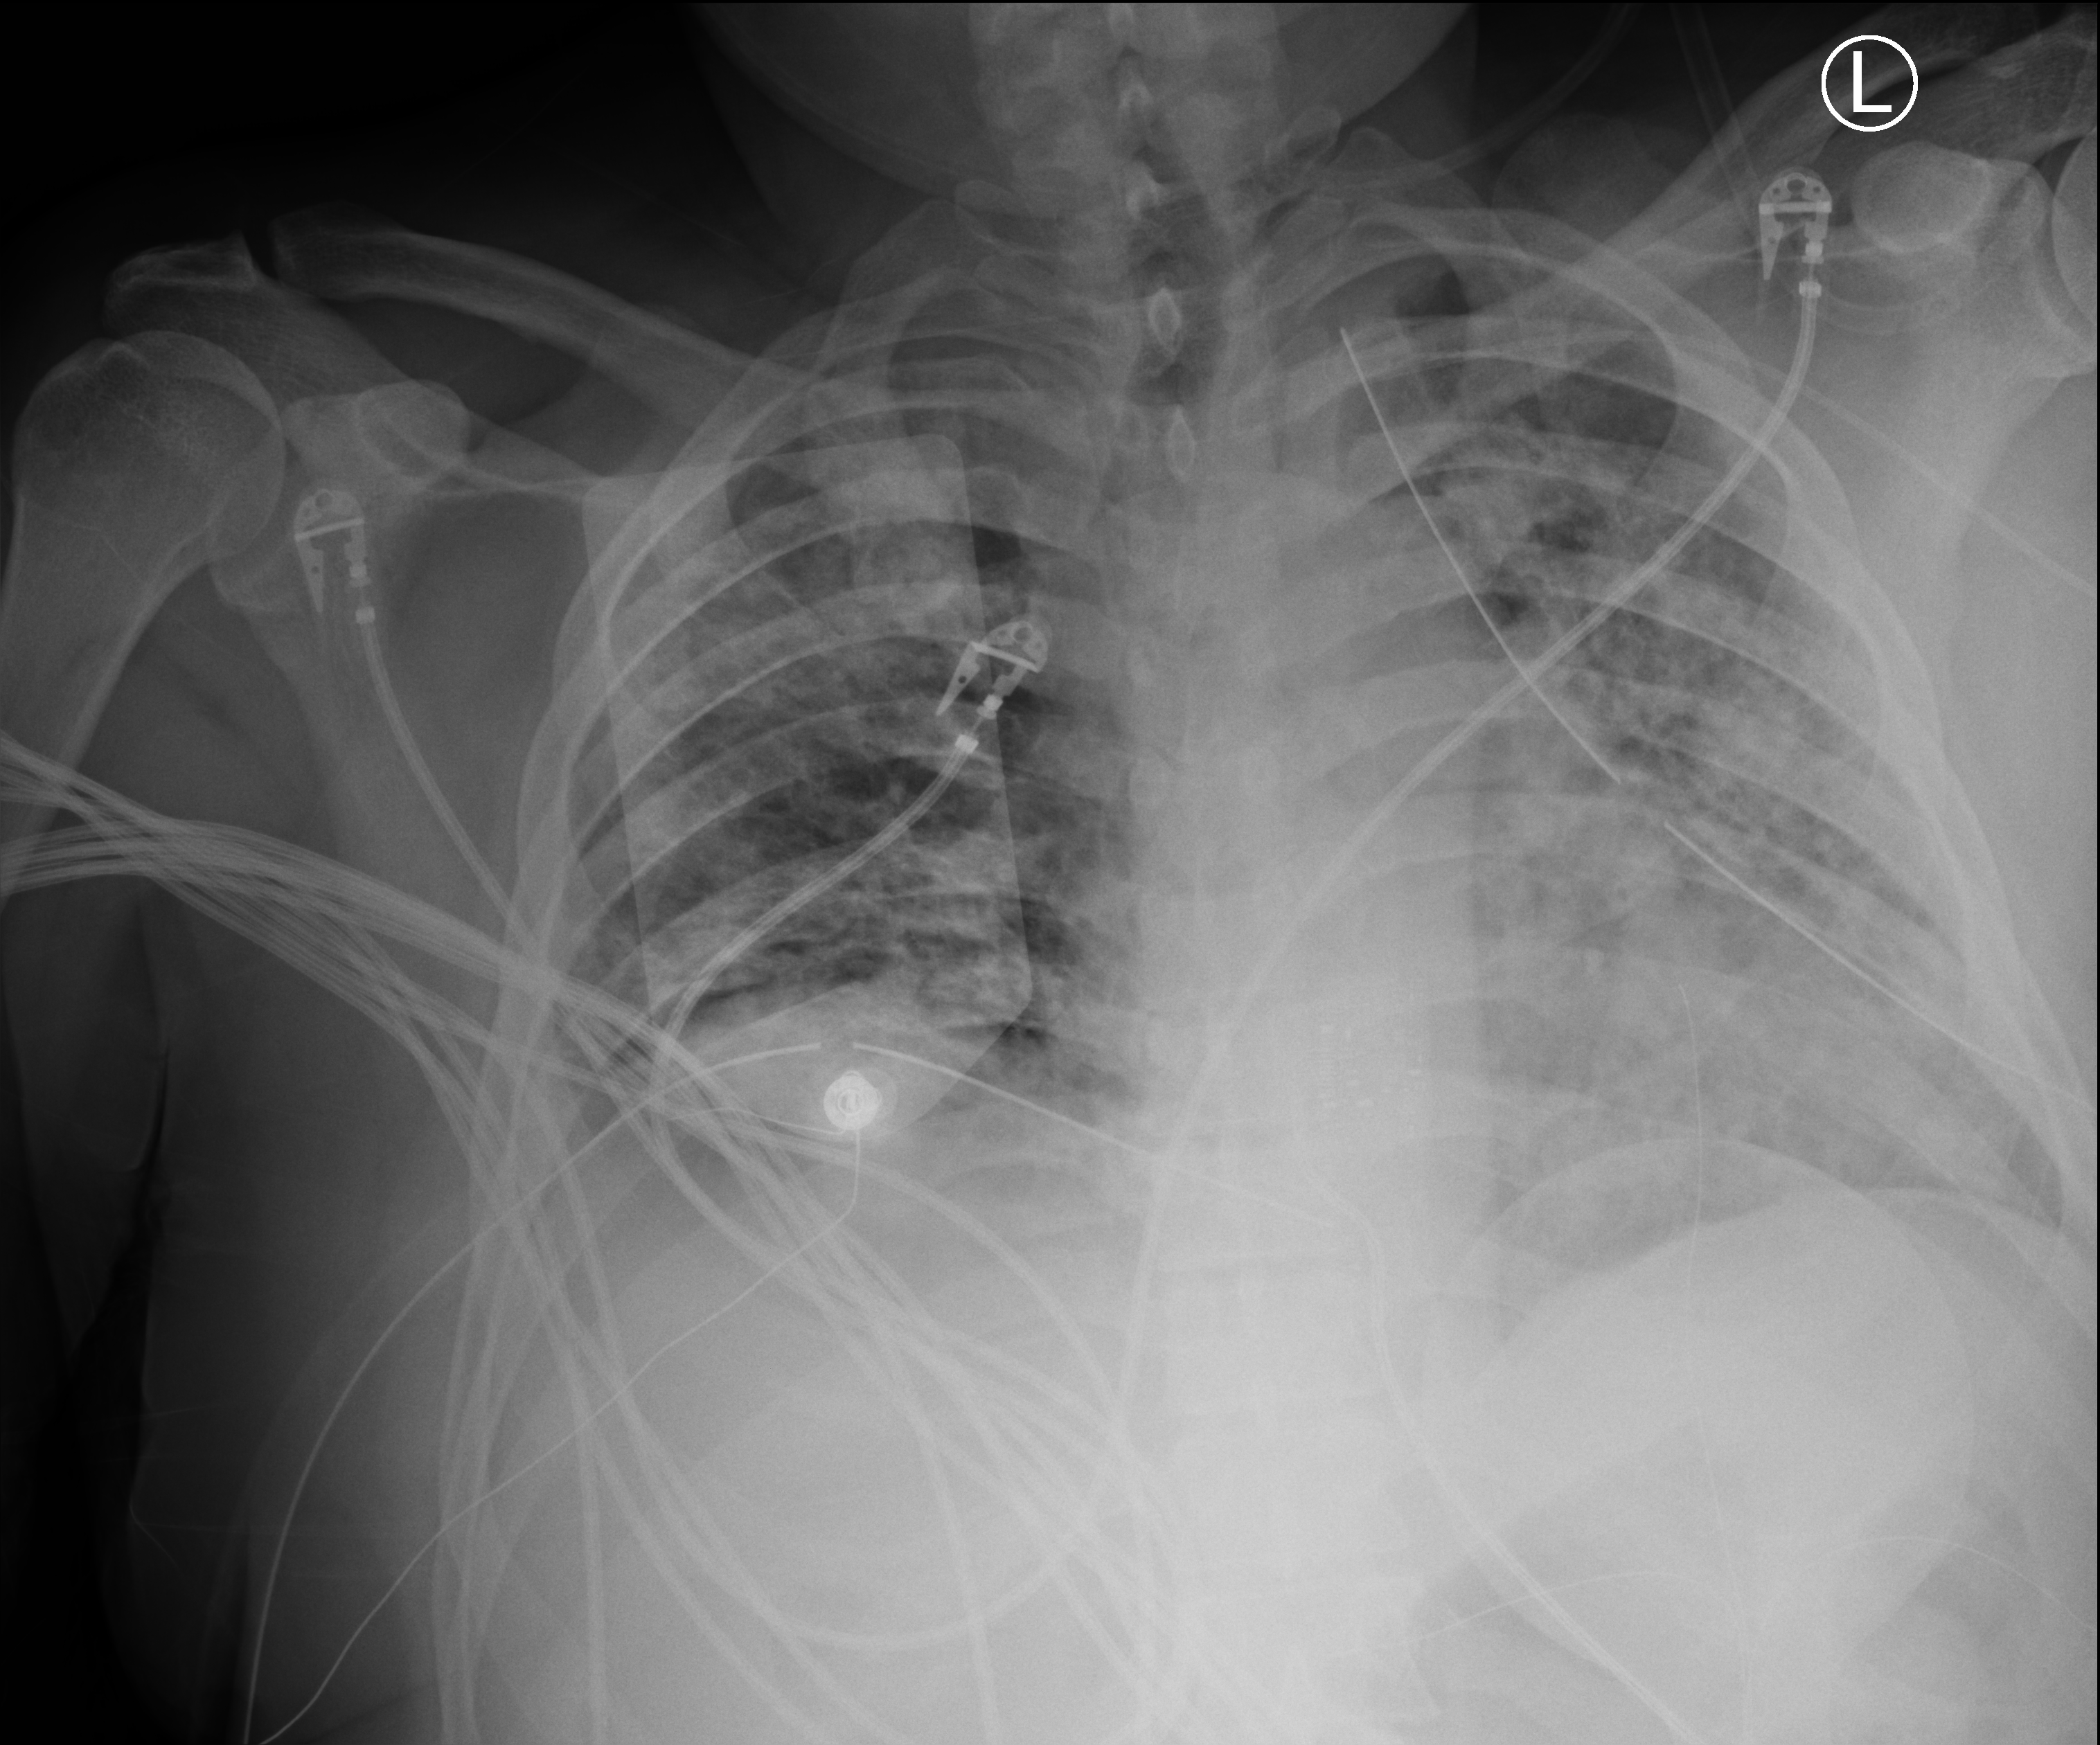
Bedside chest radiograph (computed radiography). Patient hospitalised with COVID-19; male, aged 18–59 years.
From the hospital-stay record, not from the radiograph (when in the stay this image was taken is not recorded): admitted to intensive care during this hospital stay: yes; length of hospital stay: 29 days; mechanically ventilated during this hospital stay: yes.